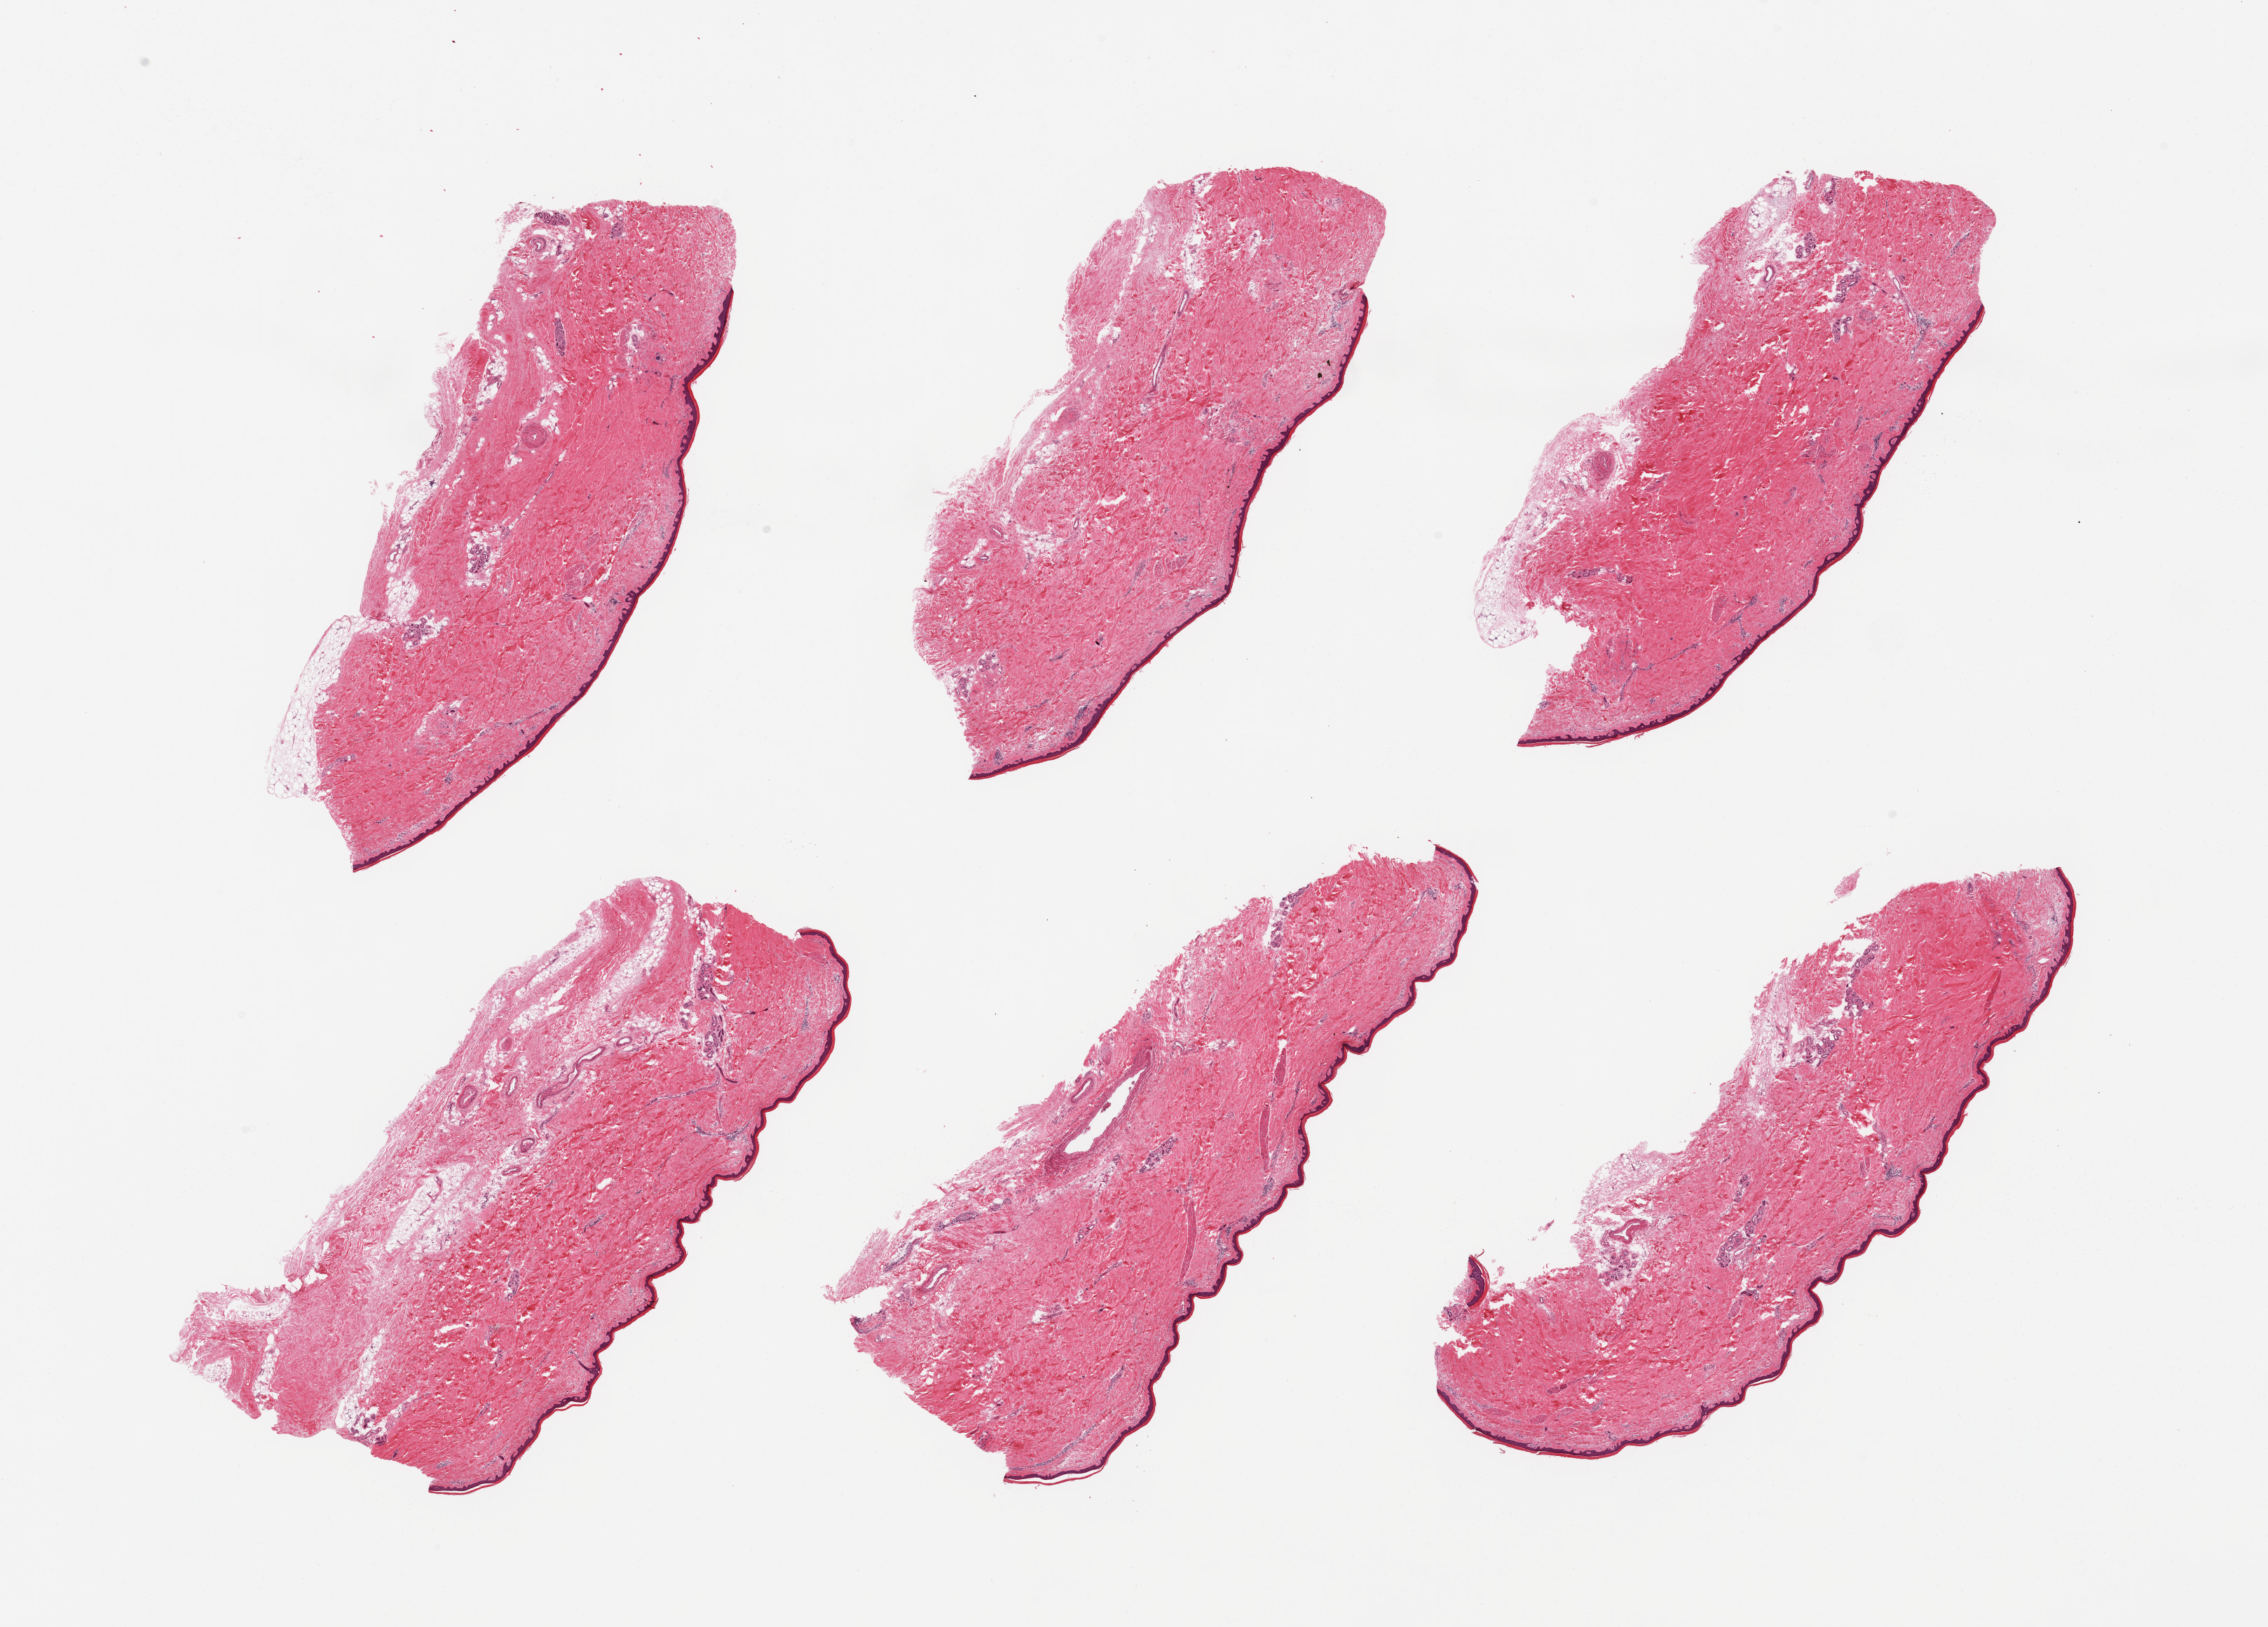
Digitized H&E-stained section, brightfield — whole scanned area (about 25.6 x 18.4 mm) shown as a low-resolution overview. PAXgene-fixed paraffin-embedded (PFPE) section. Sampled site (target tissue): skin of lower leg. Tissue donor sample. Donor: male.
Reviewer comment on this tissue sample: 6 pieces; ~10% internal/external fat; ~39 micron thick epidermis.